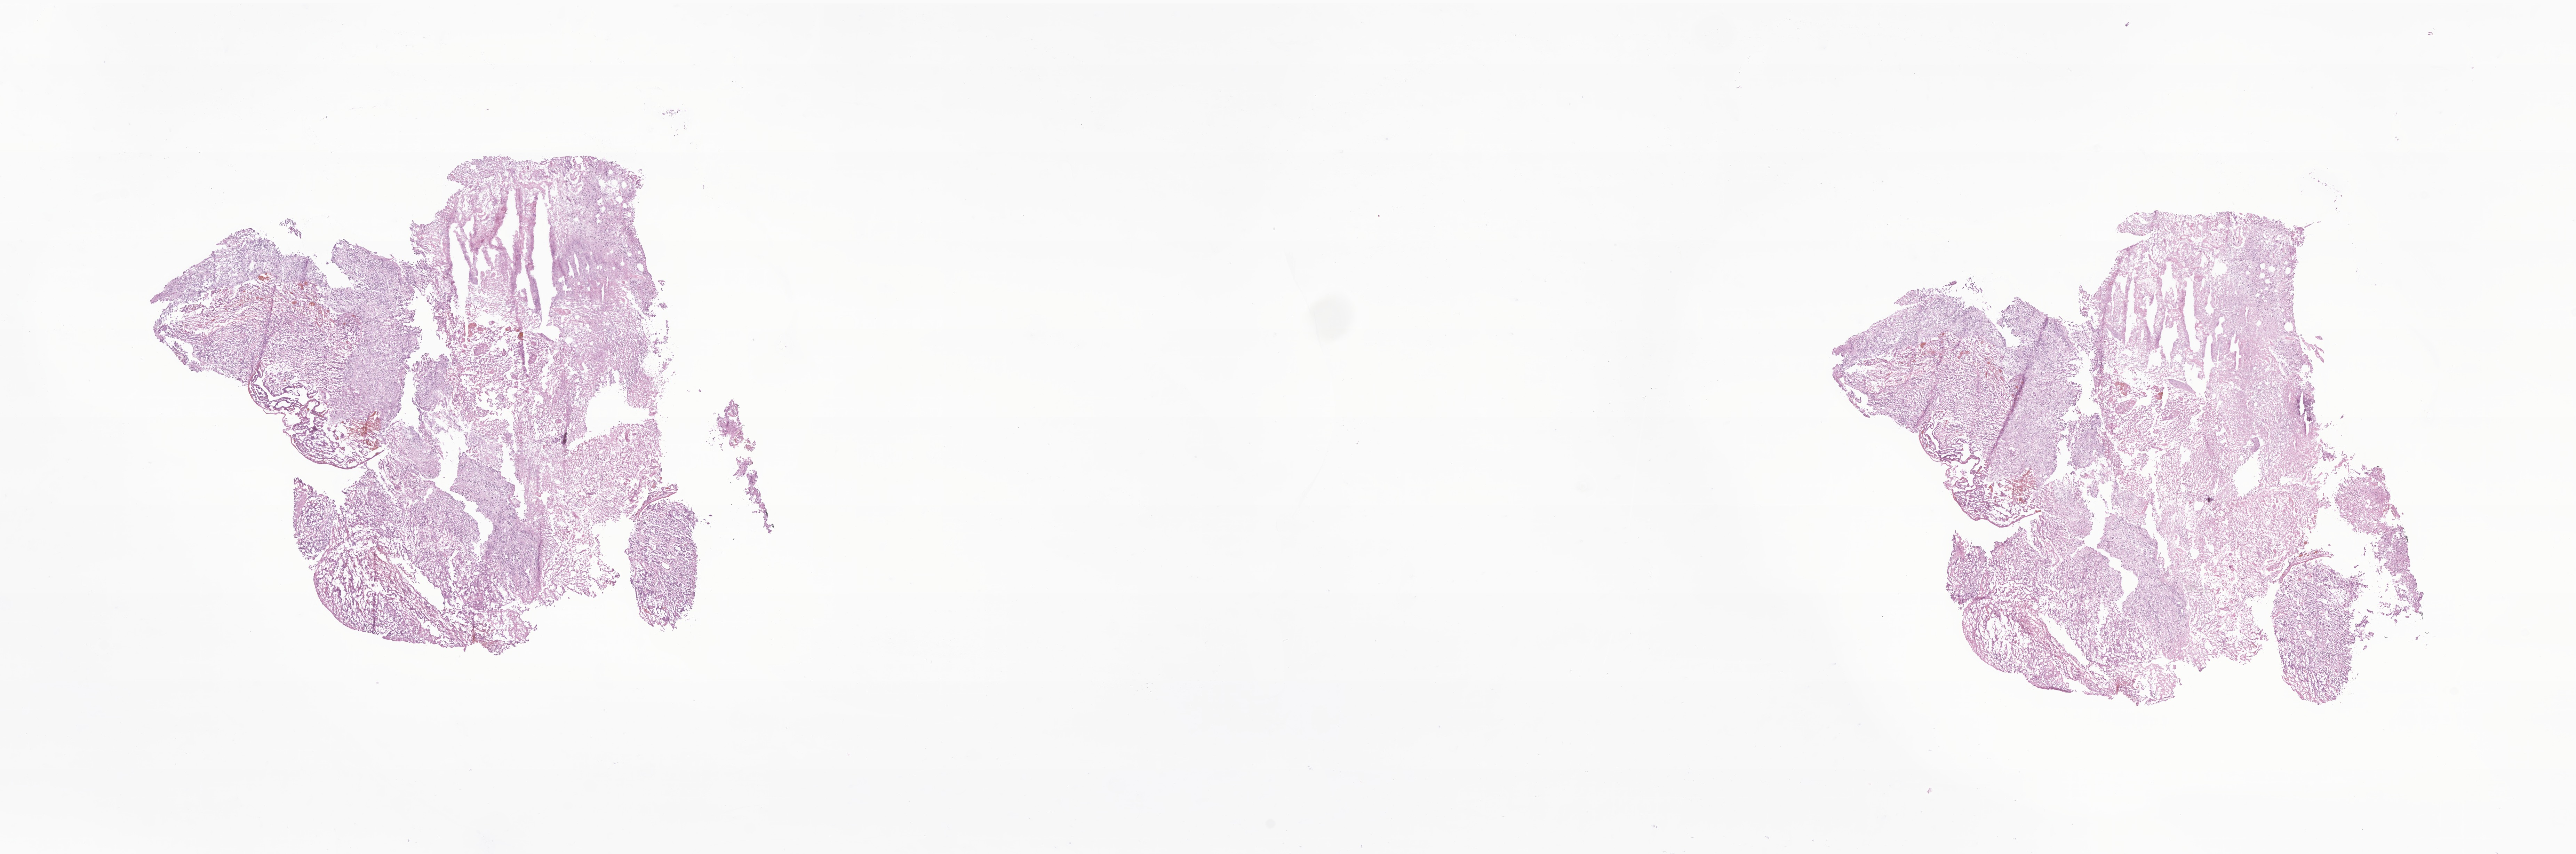
Digitized haematoxylin and eosin-stained section of tumor tissue from the brain, low-resolution overview of the scanned area, about 31.2 x 10.3 mm. Frozen section (OCT-embedded). Patient male; age 94 months (7 years 10 months).
Recorded diagnosis: Ependymoma, NOS.